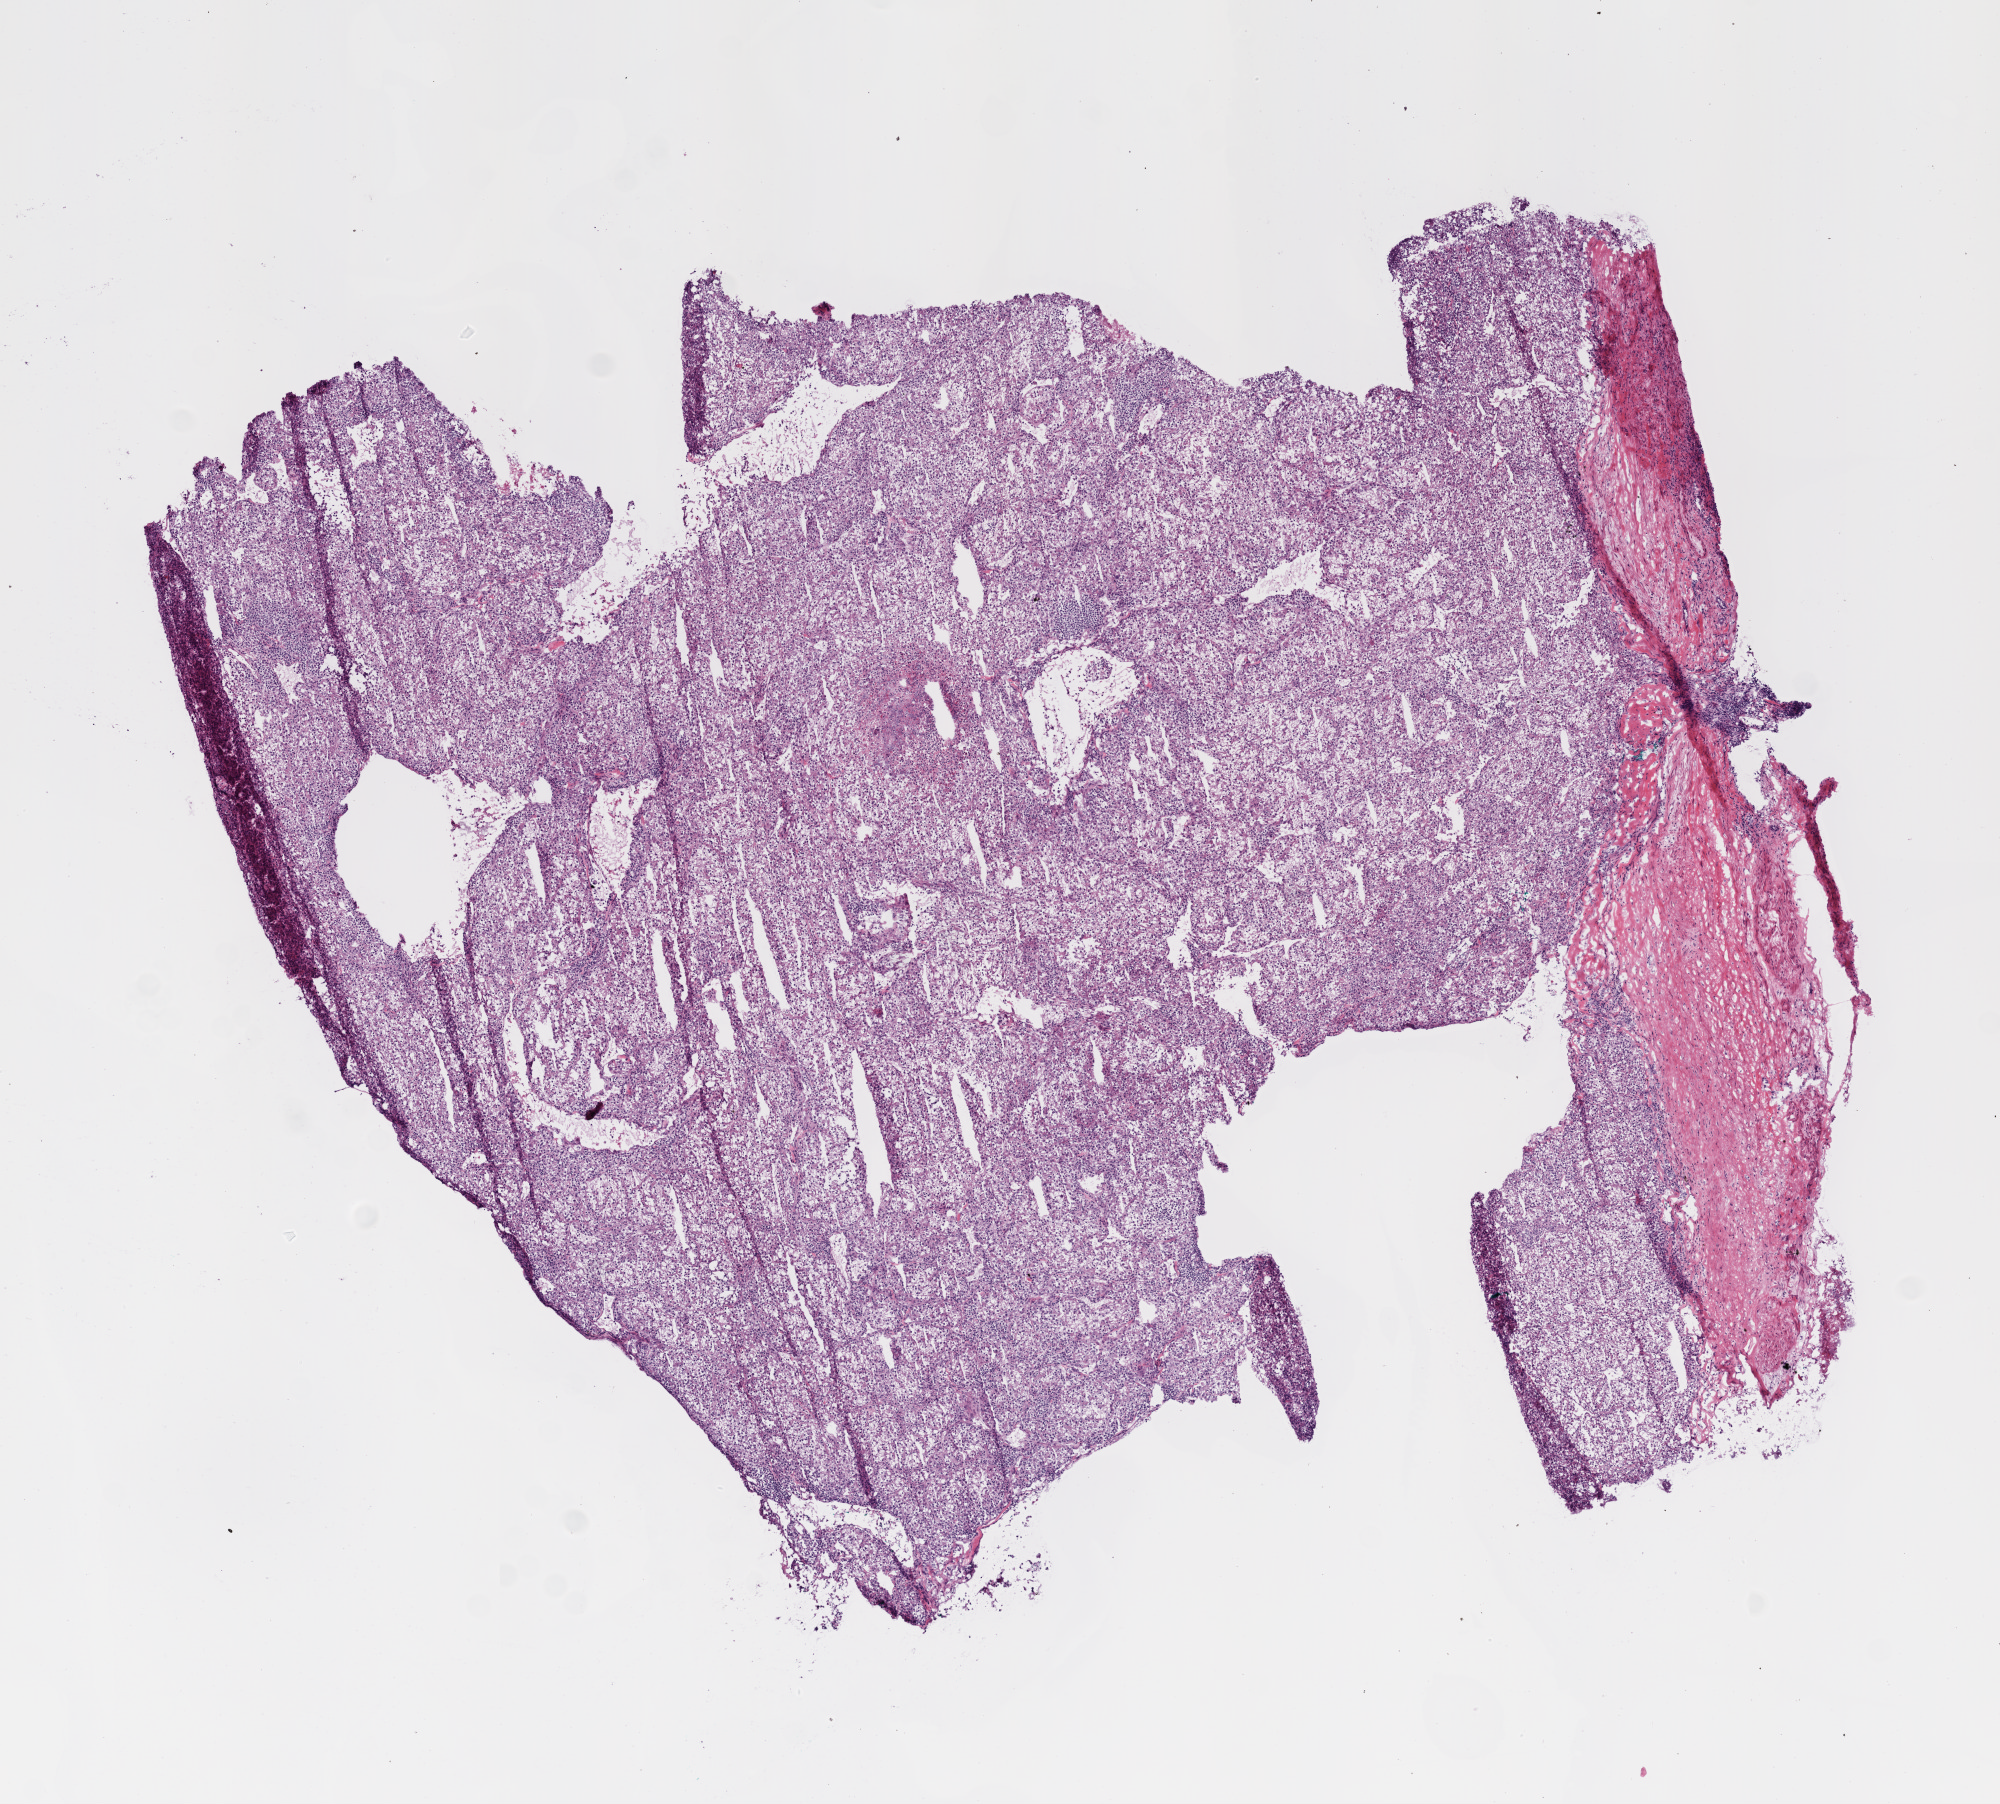
H&E-stained whole-slide image — whole scanned area (about 8.0 x 7.2 mm, slide scanned at 20x) shown as a low-resolution overview, frozen section, sample: primary tumour, kidney. Male patient; age at initial diagnosis 60 years. Histologic grade: G3 (poorly differentiated). Pathologist review of this section (percent, as recorded): tumour cells 85%, tumour nuclei 80%, normal cells 0%, stromal cells 15%, necrosis 0%.
AJCC pathologic stage: I. Diagnosis: Clear cell adenocarcinoma, NOS. Laterality: left.